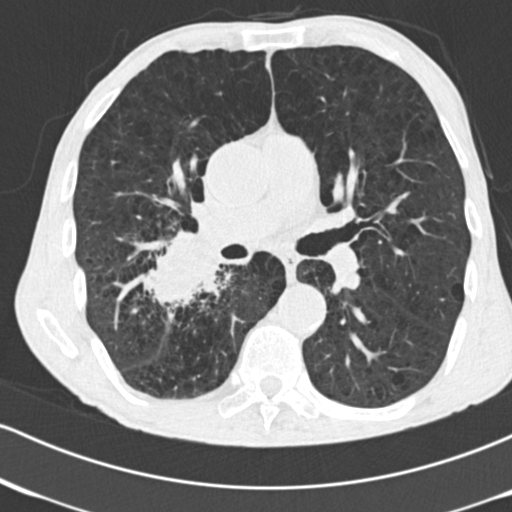
Low-dose screening chest CT, one axial slice. Position 95 of 182 along the scan axis. Lung window (W 1500 / L -600 HU). 512 × 512 image matrix, field of view 316 × 316 mm.
Annotated regions visible in this slice (manually delineated by an expert):
- lesion 1 (tumor, lower lobe of right lung): box from (x=143, y=231) to (x=222, y=307) px